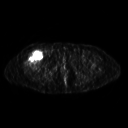
FDG PET of an extremity soft-tissue mass (from a PET/CT study), one axial slice. Position 278 of 311 along the scan axis. 3.27 mm slice thickness. 128 × 128 image matrix, field of view 500 × 500 mm. Patient: female, 57 years. Case-level facts recorded for this patient, not image findings: histological type: pleiomorphic undifferentiated sarcoma; grade: high; site of the primary tumour: right quadricep.
Outlined on this slice (expert contour drawn on MRI and transferred to this co-registered scan by the dataset authors):
- tumour plus oedema (research contour): box from (x=24, y=49) to (x=43, y=68) px
- tumour (research contour): (x=24, y=49)–(x=43, y=68)